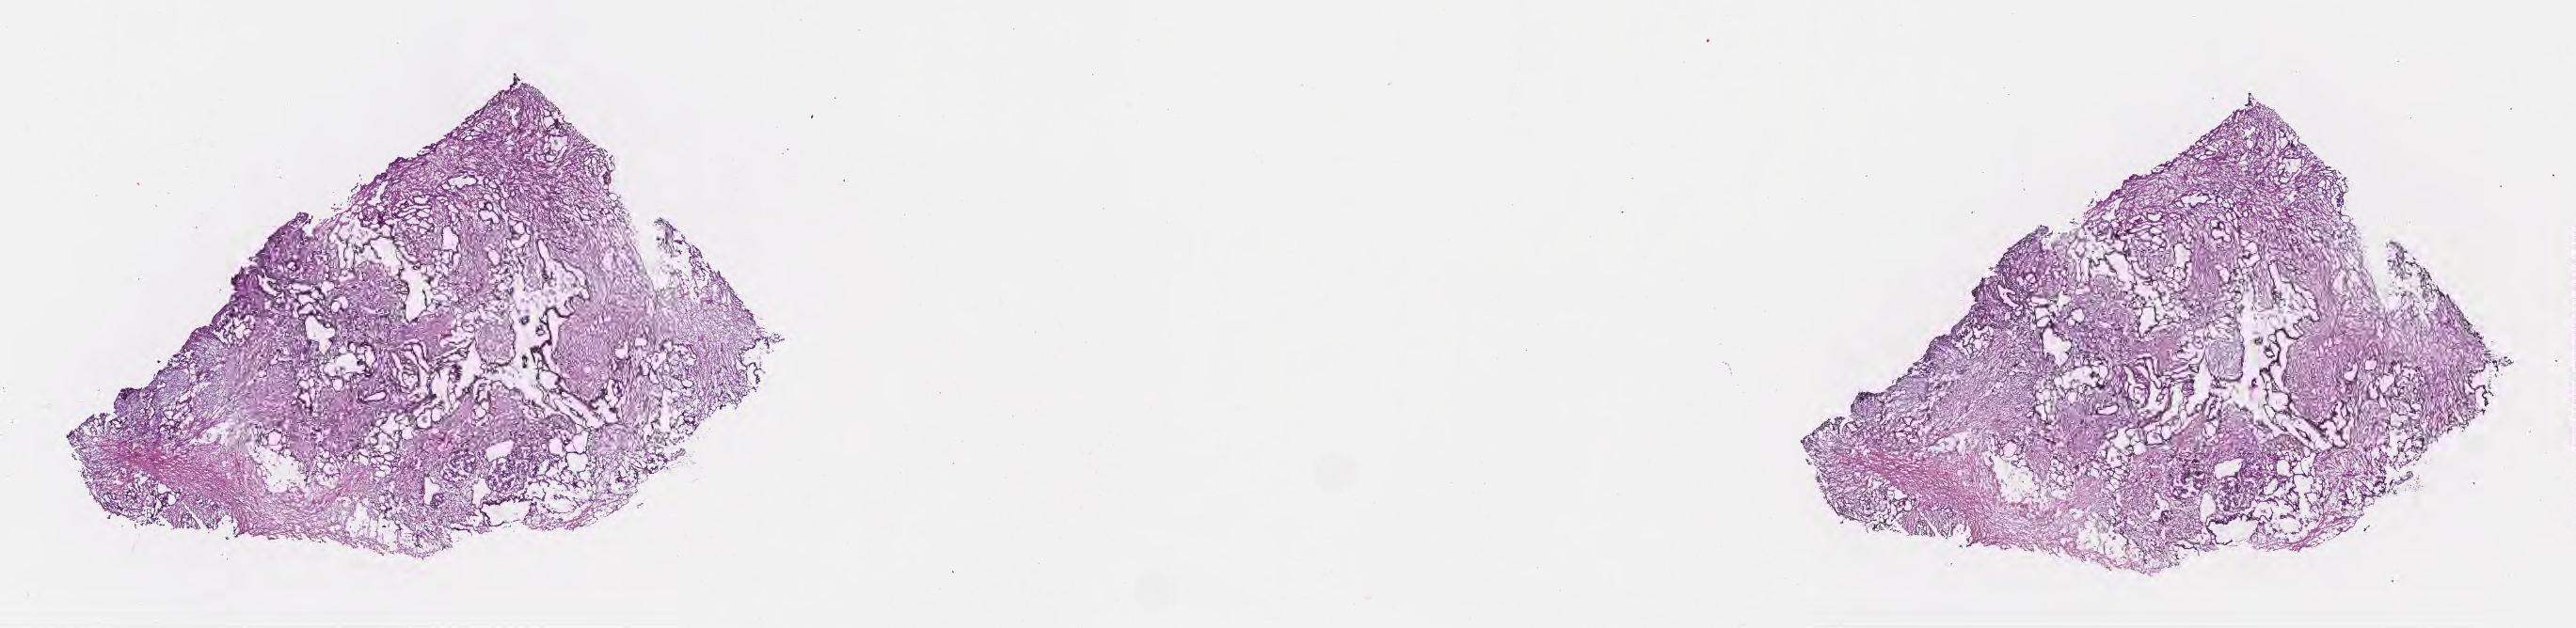
H&E whole-slide image — a low-resolution overview of the entire scanned area, about 22.1 x 5.4 mm. Frozen section (tissue freezing medium). Specimen: primary tumor. Site: head of pancreas. Male patient; age at initial diagnosis 55 years. Tumor grade: G2 (moderately differentiated). Pathologist review of this section (percent, as recorded): tumor cells 48%, tumor nuclei 85%, stromal cells 51%, necrosis 1%, normal cells 0%. Infiltration values recorded for this section: lymphocyte infiltration 10%, monocyte infiltration 1%, neutrophil infiltration 0%.
Diagnosis: Infiltrating duct carcinoma, NOS. AJCC pathologic stage: Stage III. Section: top of the tissue portion.